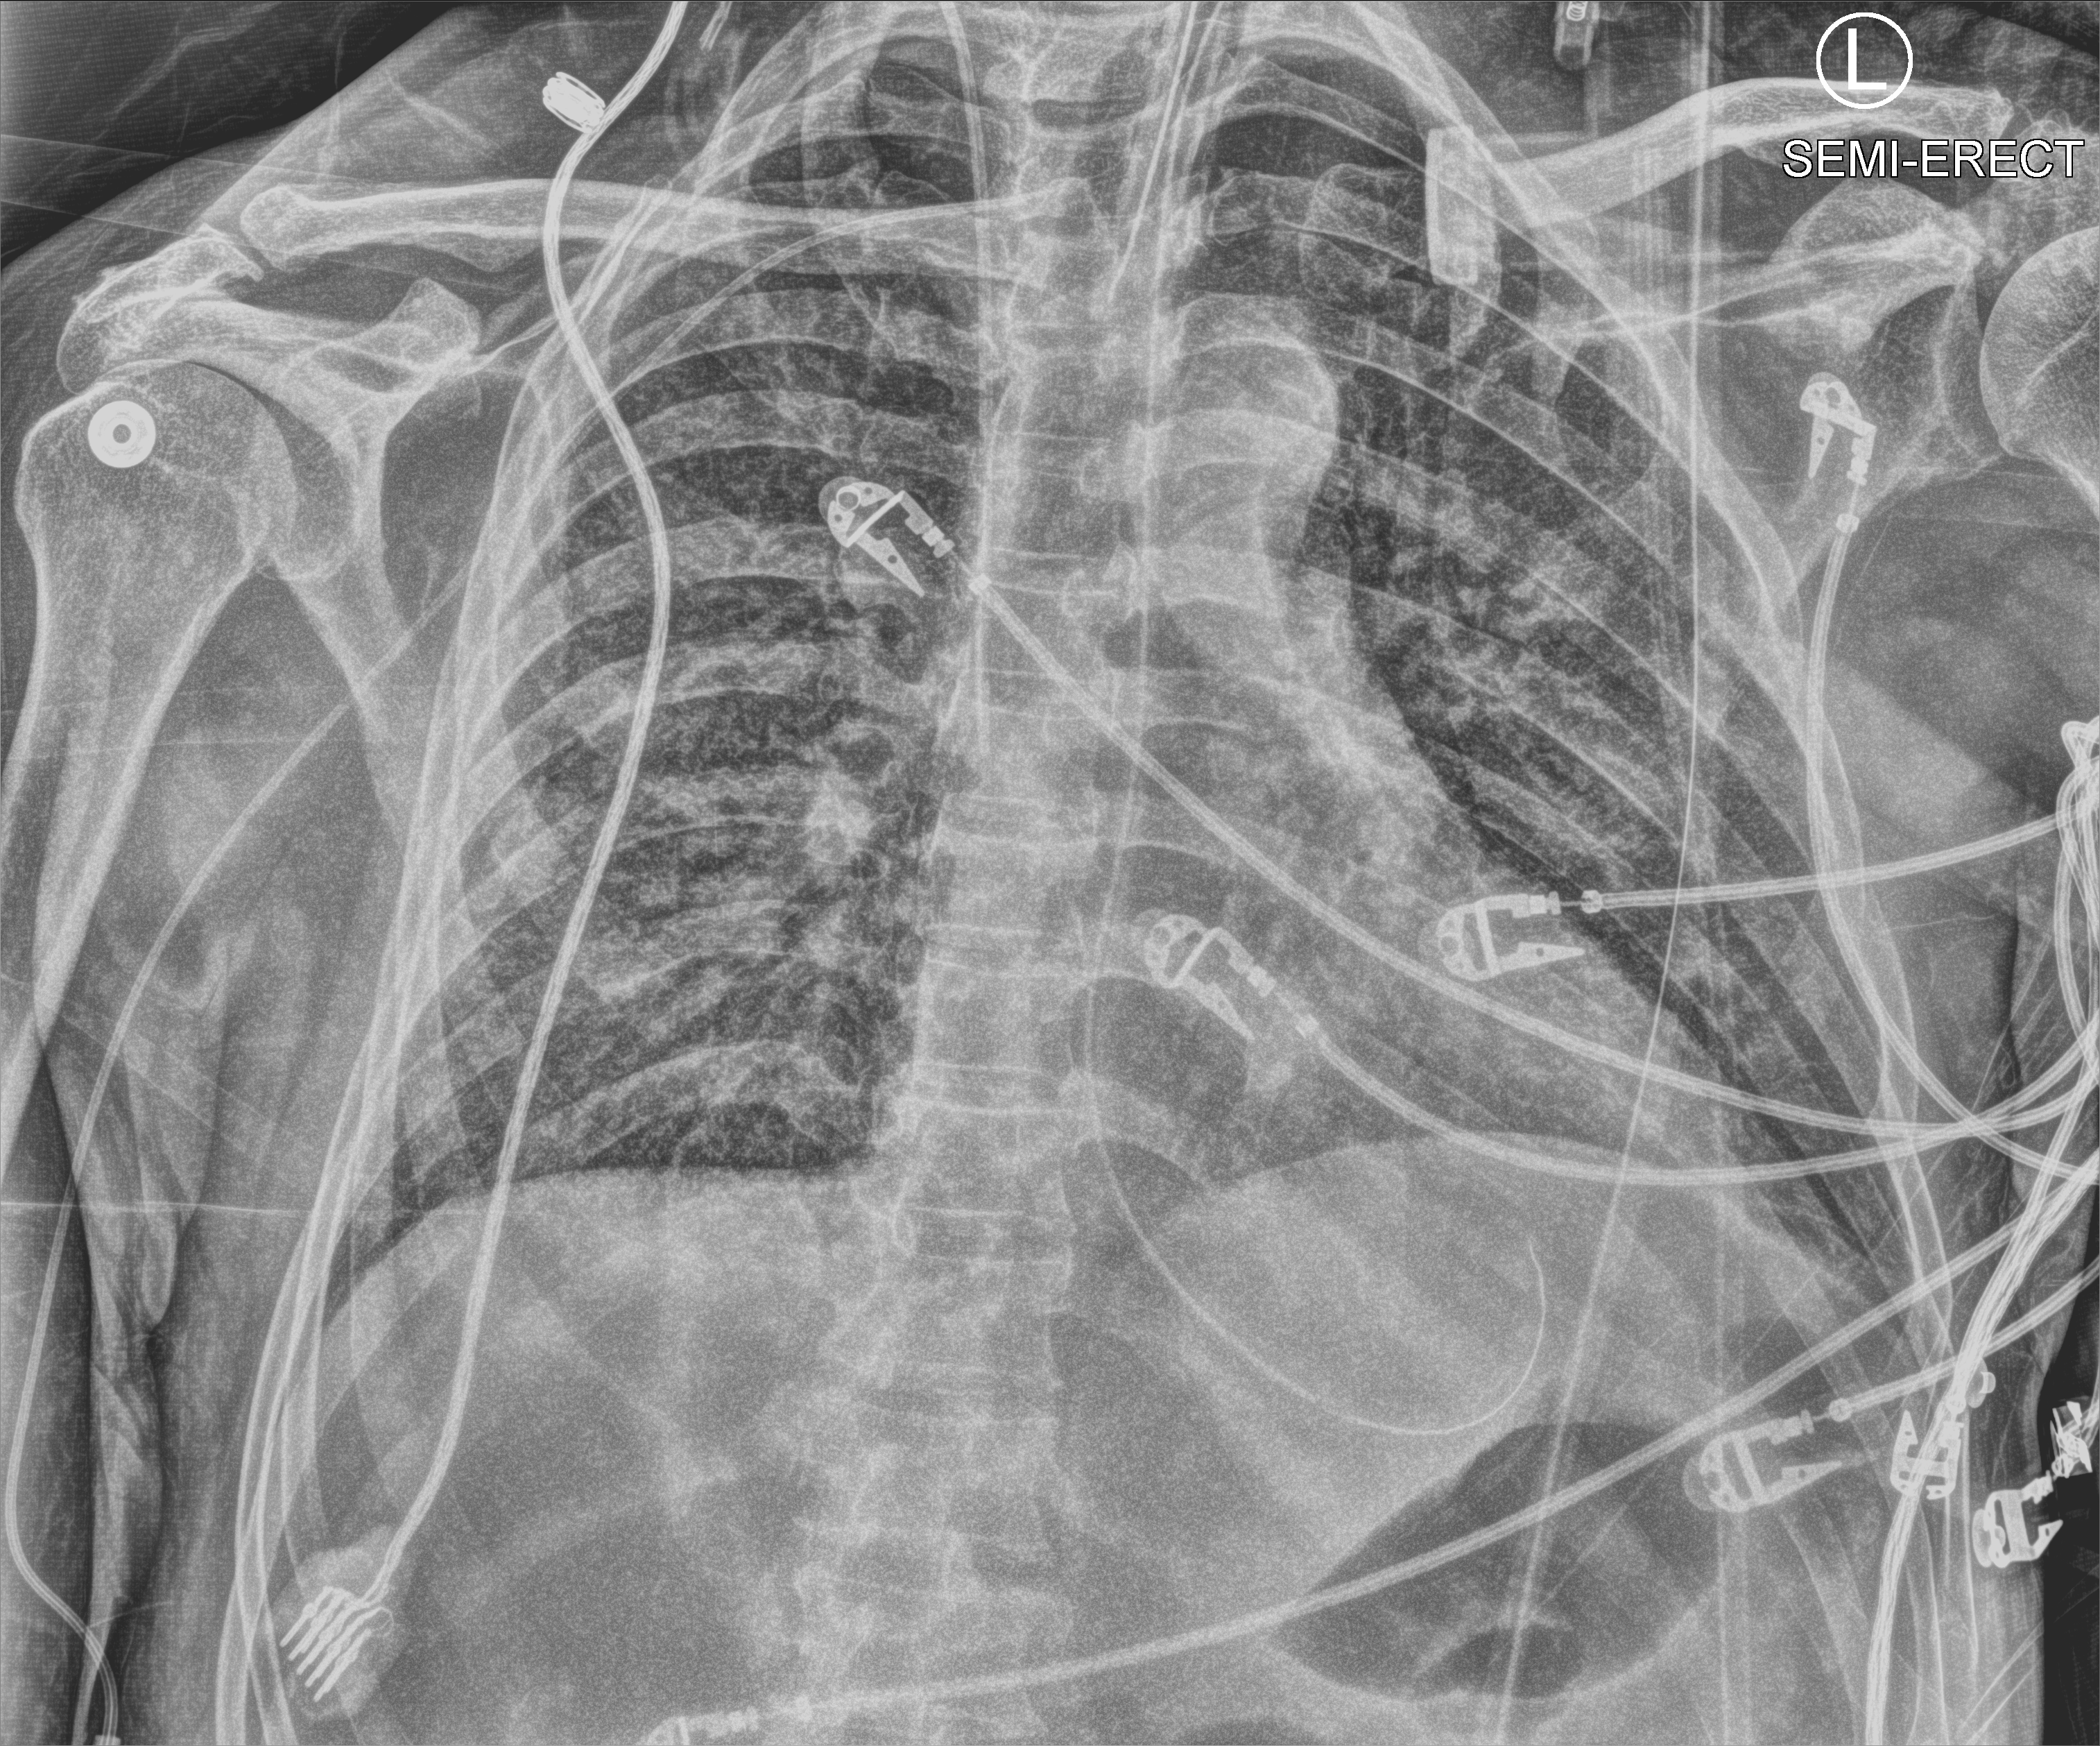
Portable chest radiograph; anteroposterior (AP) projection. Male patient hospitalised with COVID-19, age 60–74 years.
From the hospital-stay record, not from the radiograph (when in the stay this image was taken is not recorded):
- admitted to intensive care during this hospital stay: yes